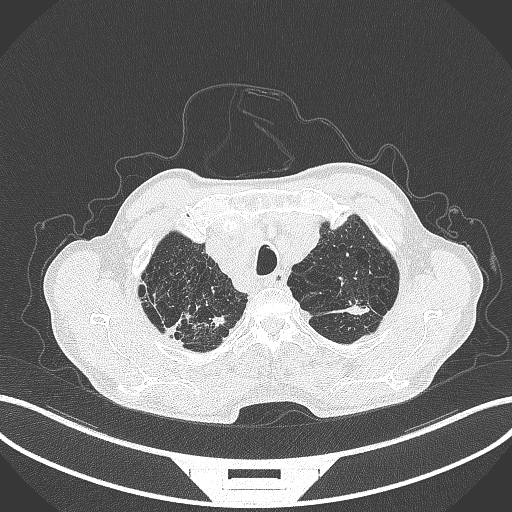
Chest CT, one axial slice; position 389 of 463 along the scan axis; reconstruction kernel B70f; 120 kVp; lung window (W 1500 / L -600 HU); 512 × 512 image matrix, field of view 400 × 400 mm. Male patient, age 74 years. Case-level facts recorded for this patient, not image findings: clinical TNM (as recorded): T2a N1 M0.
Annotated regions visible in this slice (bounding box drawn by a radiologist):
- lung tumour (recorded histology: adenocarcinoma): bounding box <326,301,374,316> (left, top, right, bottom; pixels)